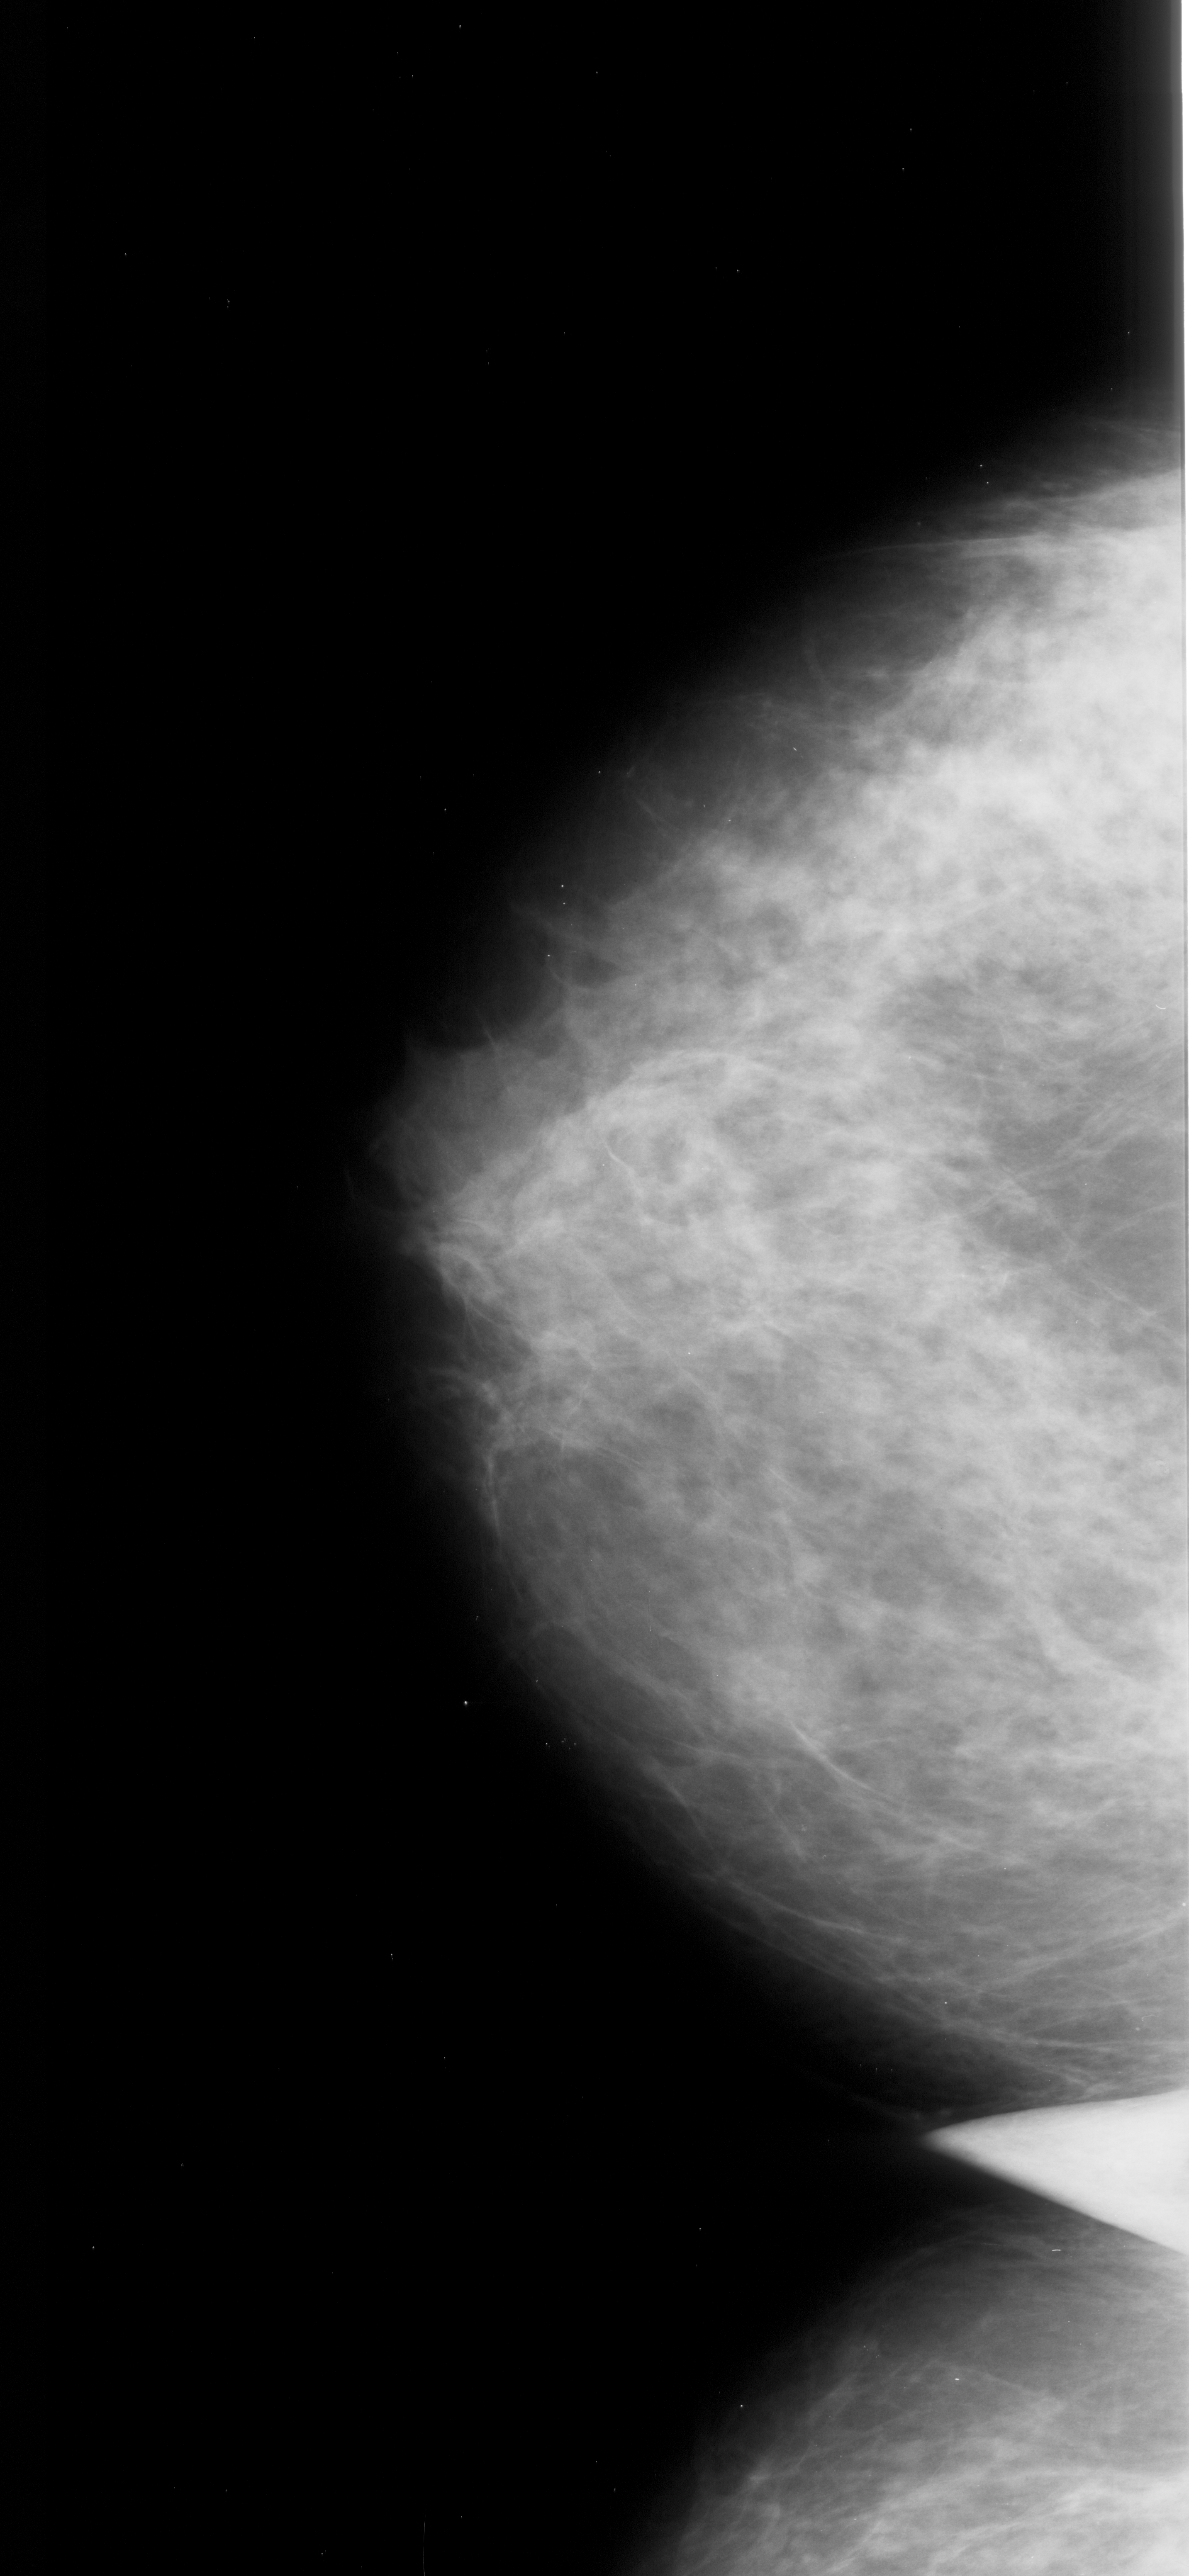
Digitized screen-film mammogram. Left breast. CC view. BI-RADS breast density category 3 (scale 1–4). 1189 × 2576 image matrix.
Expert-marked regions of interest on this film, with their recorded descriptors:
- calcifications, morphology pleomorphic, distribution clustered; BI-RADS assessment category 4; pathology result (as recorded, not read from the image): malignant: bounding box [x1, y1, x2, y2] px = [917, 1234, 1039, 1314]